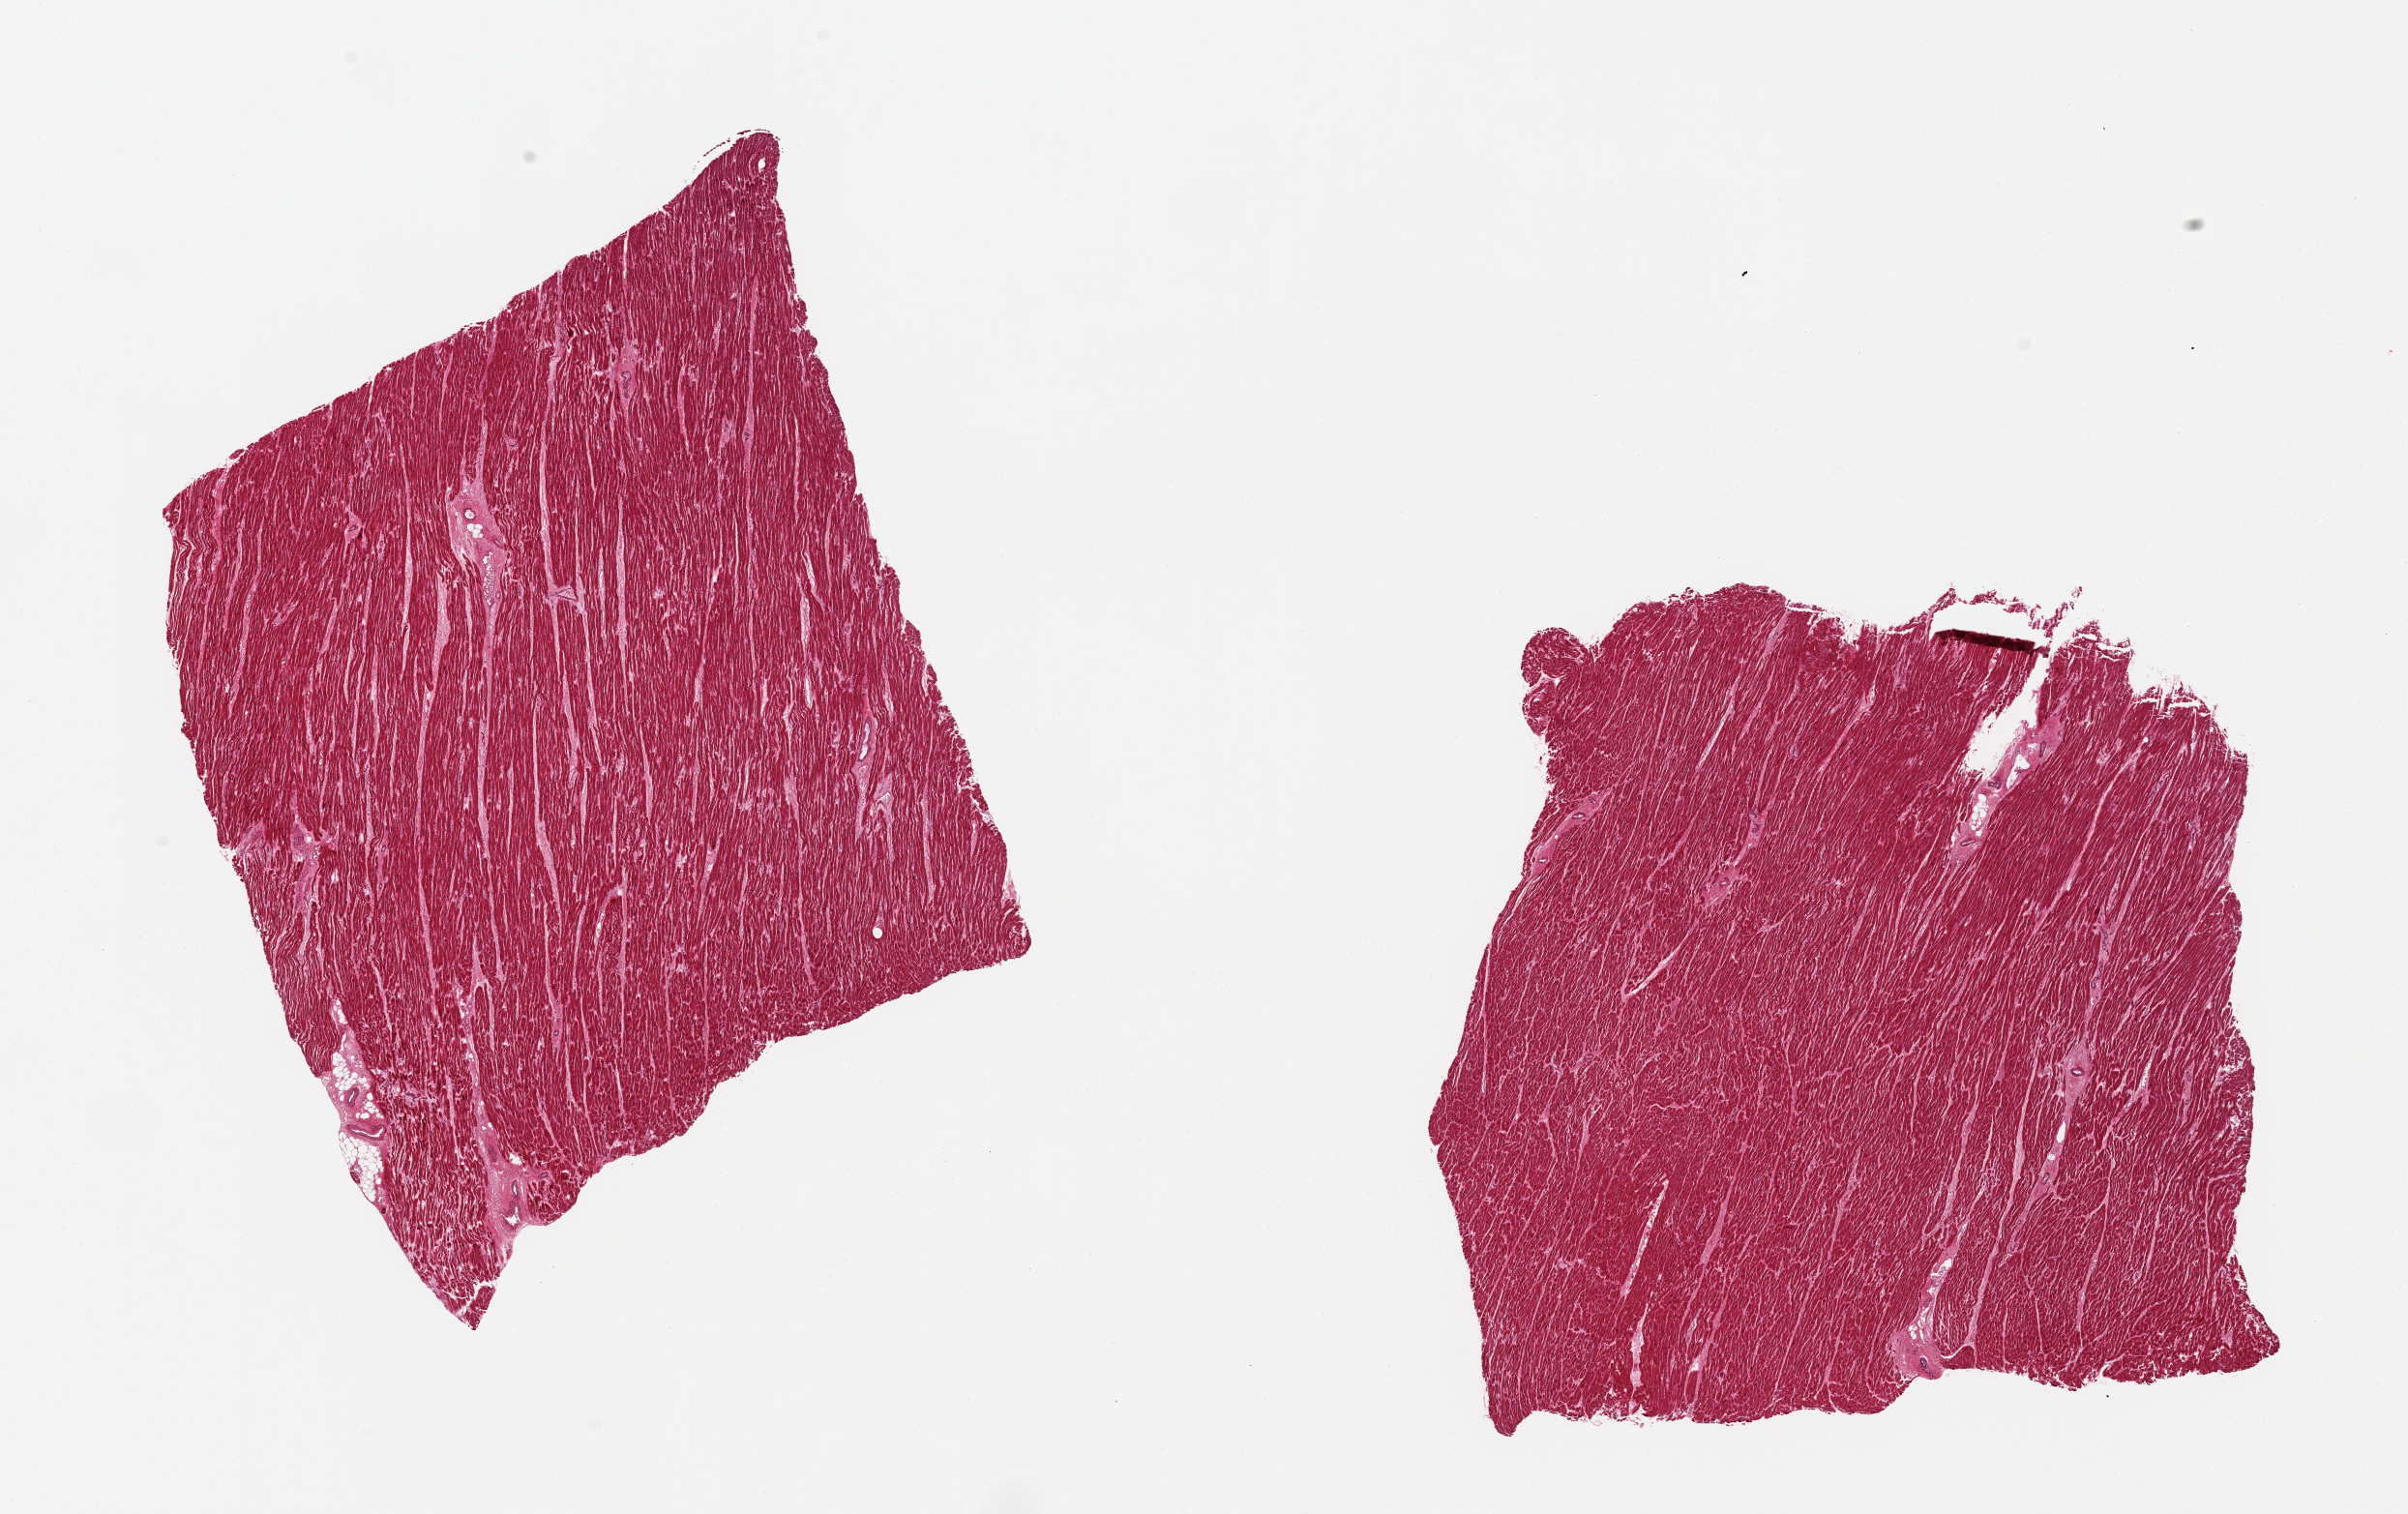
Digitized hematoxylin and eosin (H&E)-stained section — low-resolution overview of the scanned area, about 19.7 x 12.4 mm (slide scanned at 20x); PAXgene-fixed, paraffin-embedded tissue; target tissue: heart; donor tissue sample. Female donor.
Pathologist's review note for this sample: 2 pieces, minimal ischemic changes.